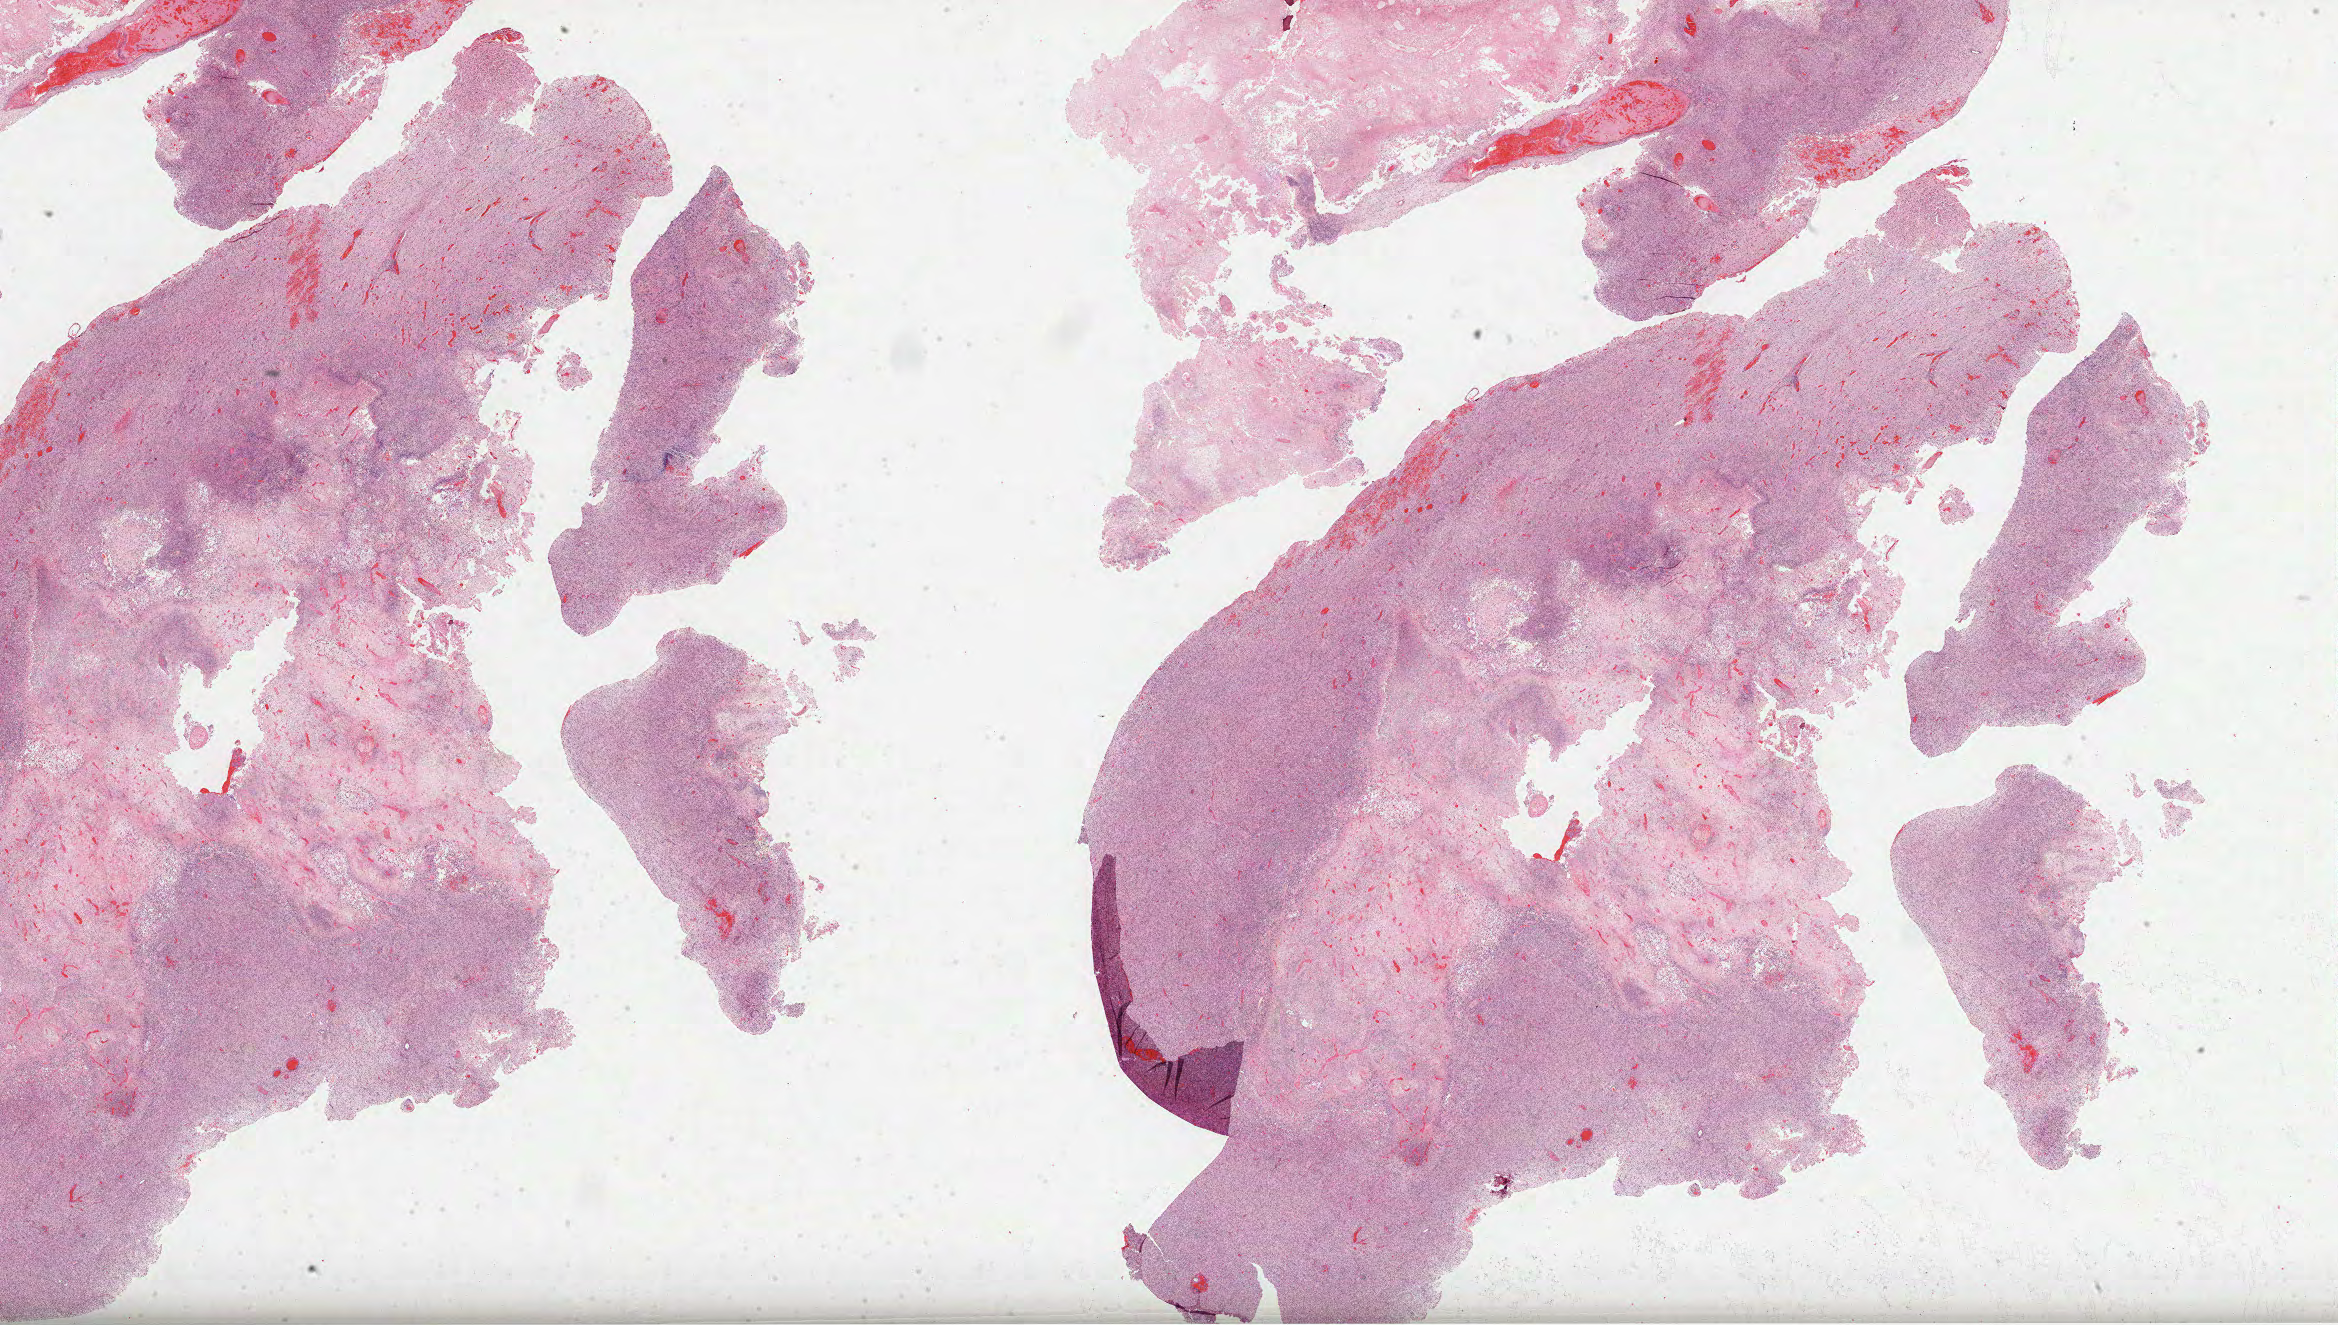
Digitized H&E-stained tissue section (whole slide), a low-resolution overview of the entire scanned area, about 37.7 x 21.4 mm. Formalin-fixed paraffin-embedded (FFPE) diagnostic section. Brain, primary tumour sample. Patient: male, age at initial diagnosis 58 years.
• pathologic diagnosis: Glioblastoma